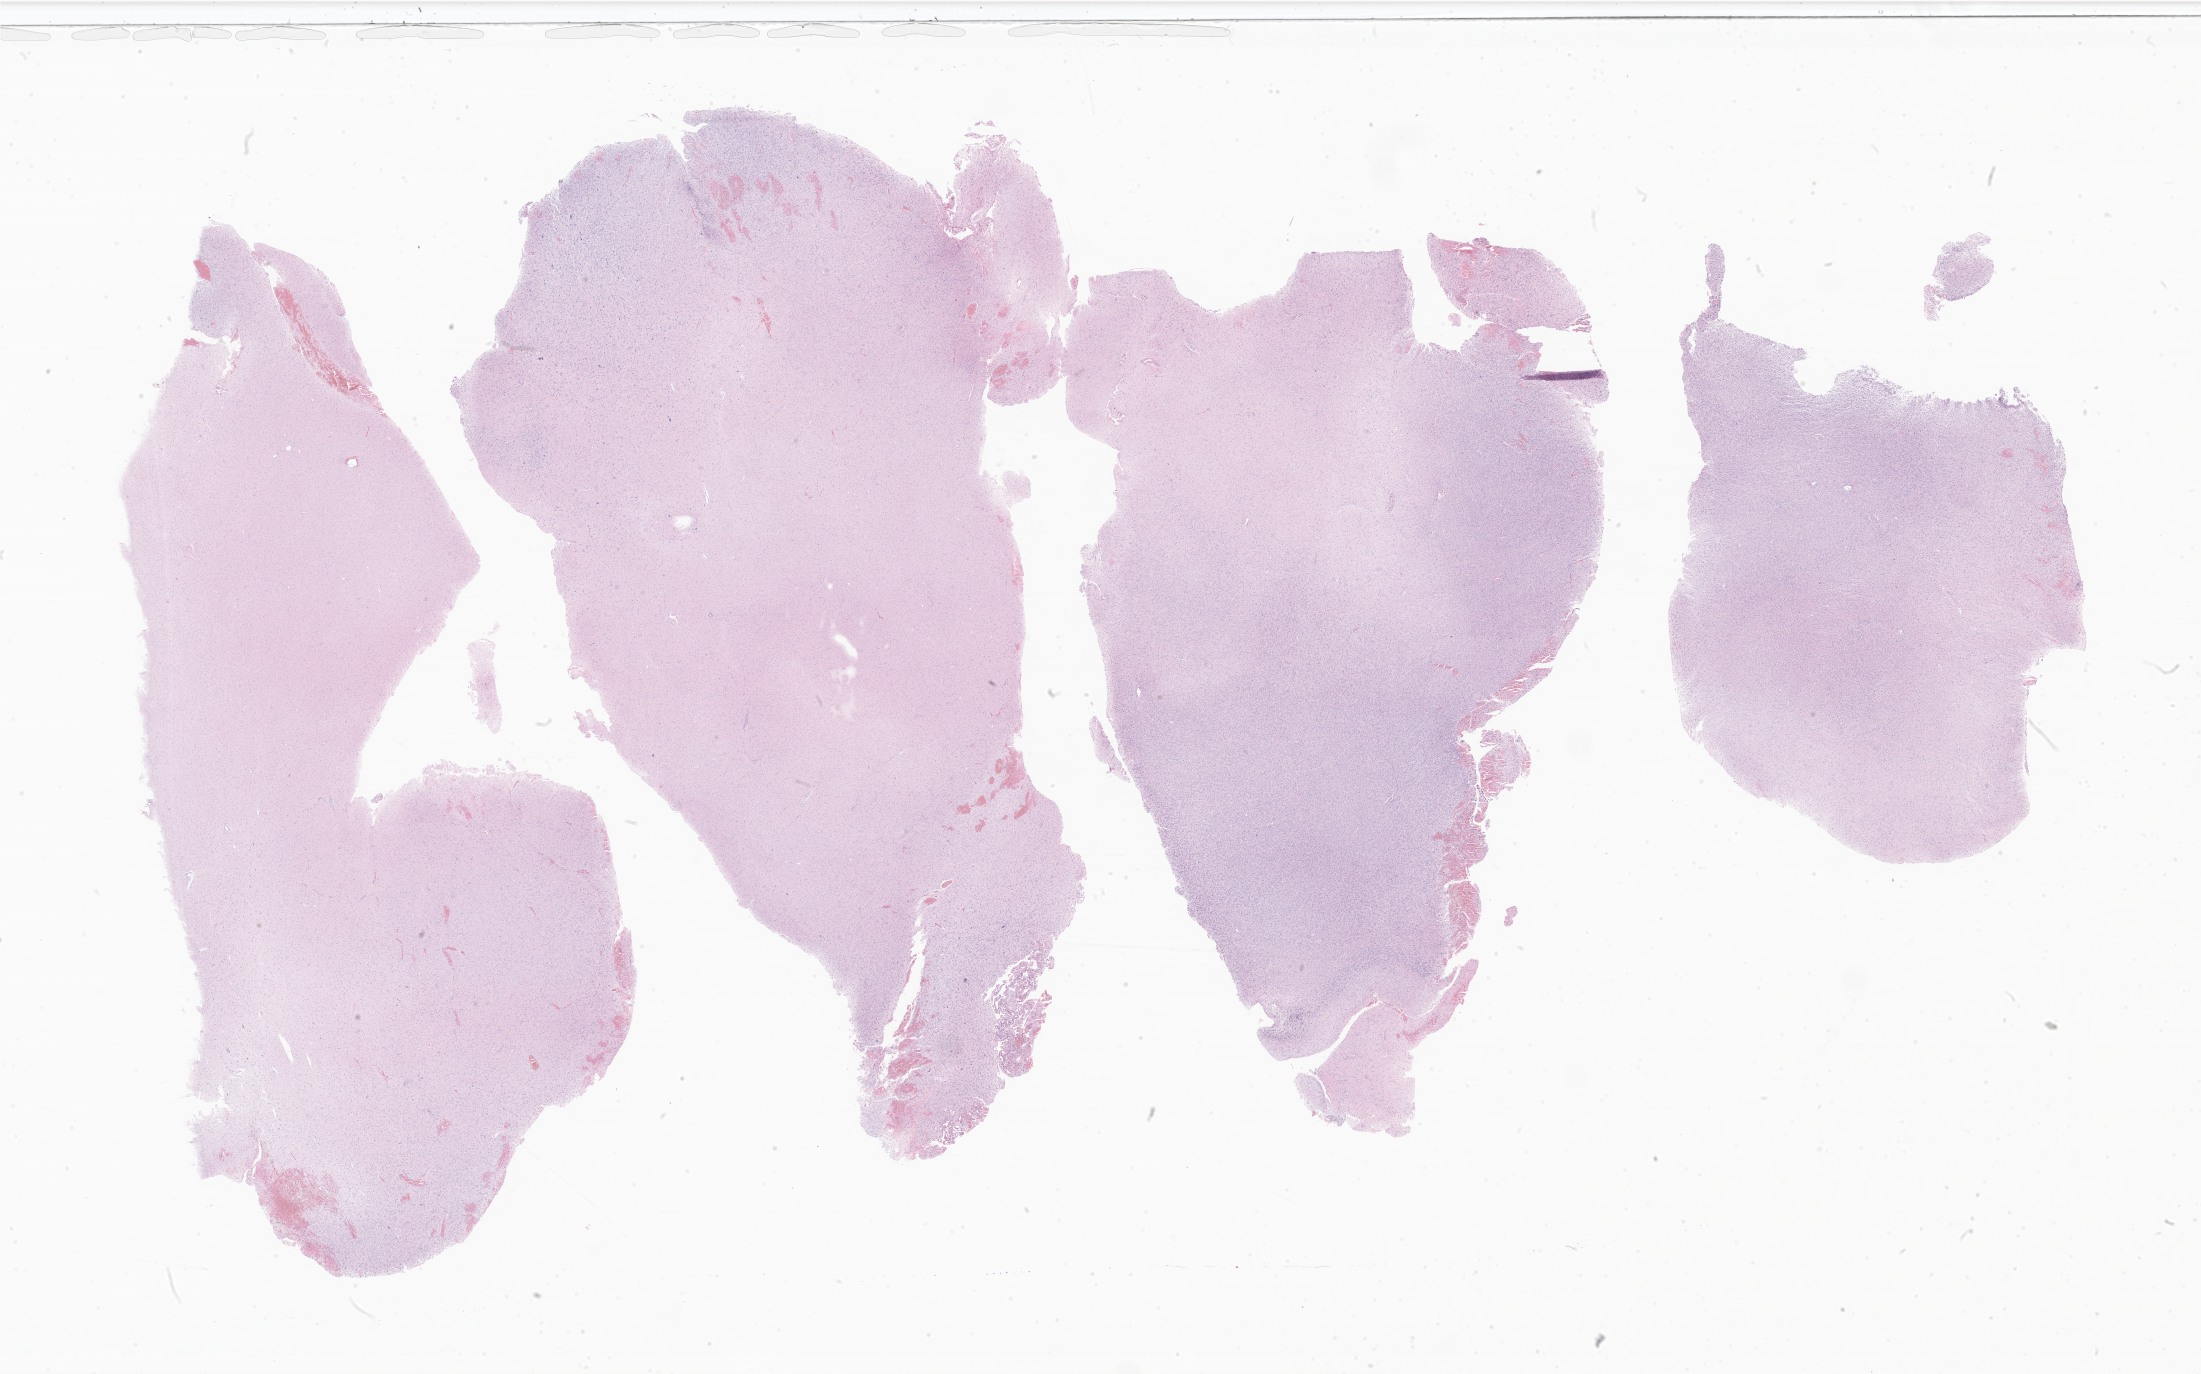
Whole-slide image, H&E stain of tumor tissue from the cerebellum — a low-resolution overview of the entire scanned area, about 37.1 x 23.2 mm; FFPE section. Female patient, age 111 months (9 years 3 months).
Diagnosis: Glioma, malignant.